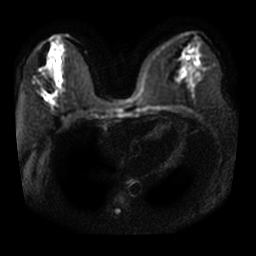
Breast MRI, one axial slice. Position 17 of 32 along the scan axis. Diffusion-weighted series; image 2 of 4 stored at this slice position (different b-values; order by instance number). 3 T. 5 mm slice thickness. 256 × 256 image matrix, field of view 340 × 340 mm. Female patient.
Annotated regions visible in this slice (manually delineated by an expert):
- tumour on diffusion-weighted imaging: bounding box <51,99,53,103> (left, top, right, bottom; pixels)